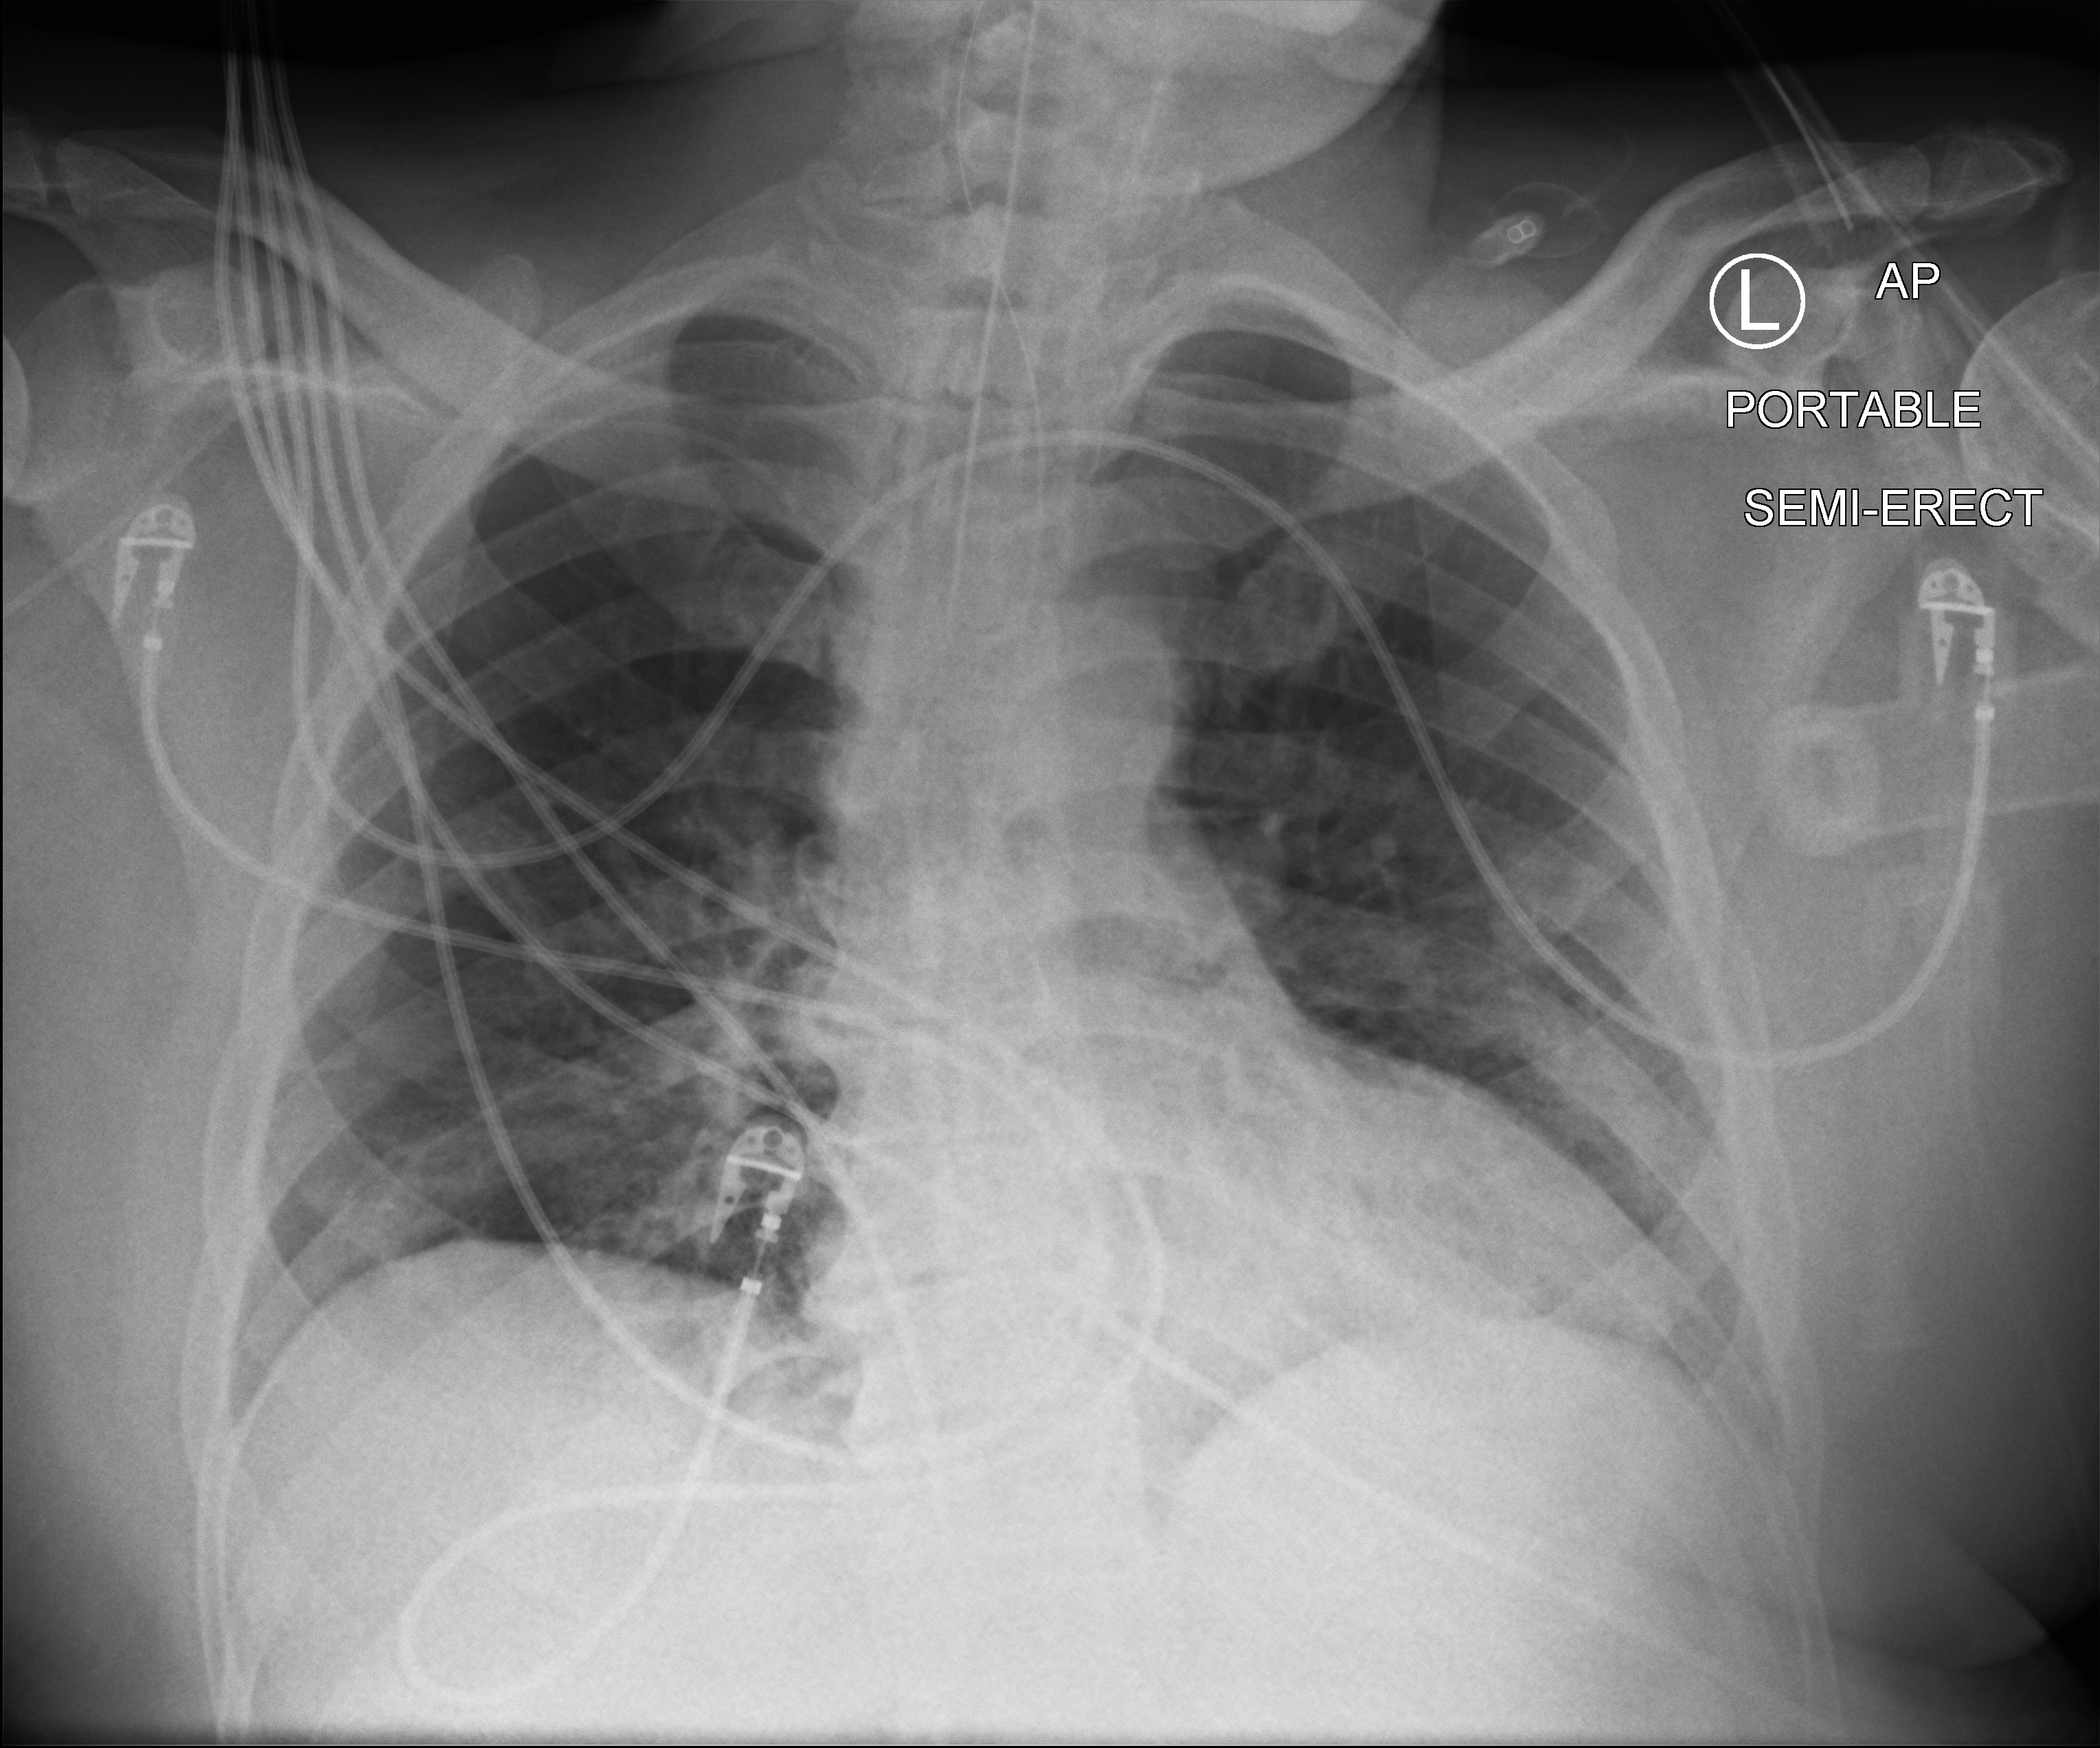
Portable chest radiograph; anteroposterior (AP) projection. Male patient hospitalised with COVID-19, age 18–59 years.
Admission-level facts for this patient (not findings on this image; timing relative to this image not recorded): mechanically ventilated during this hospital stay: yes.